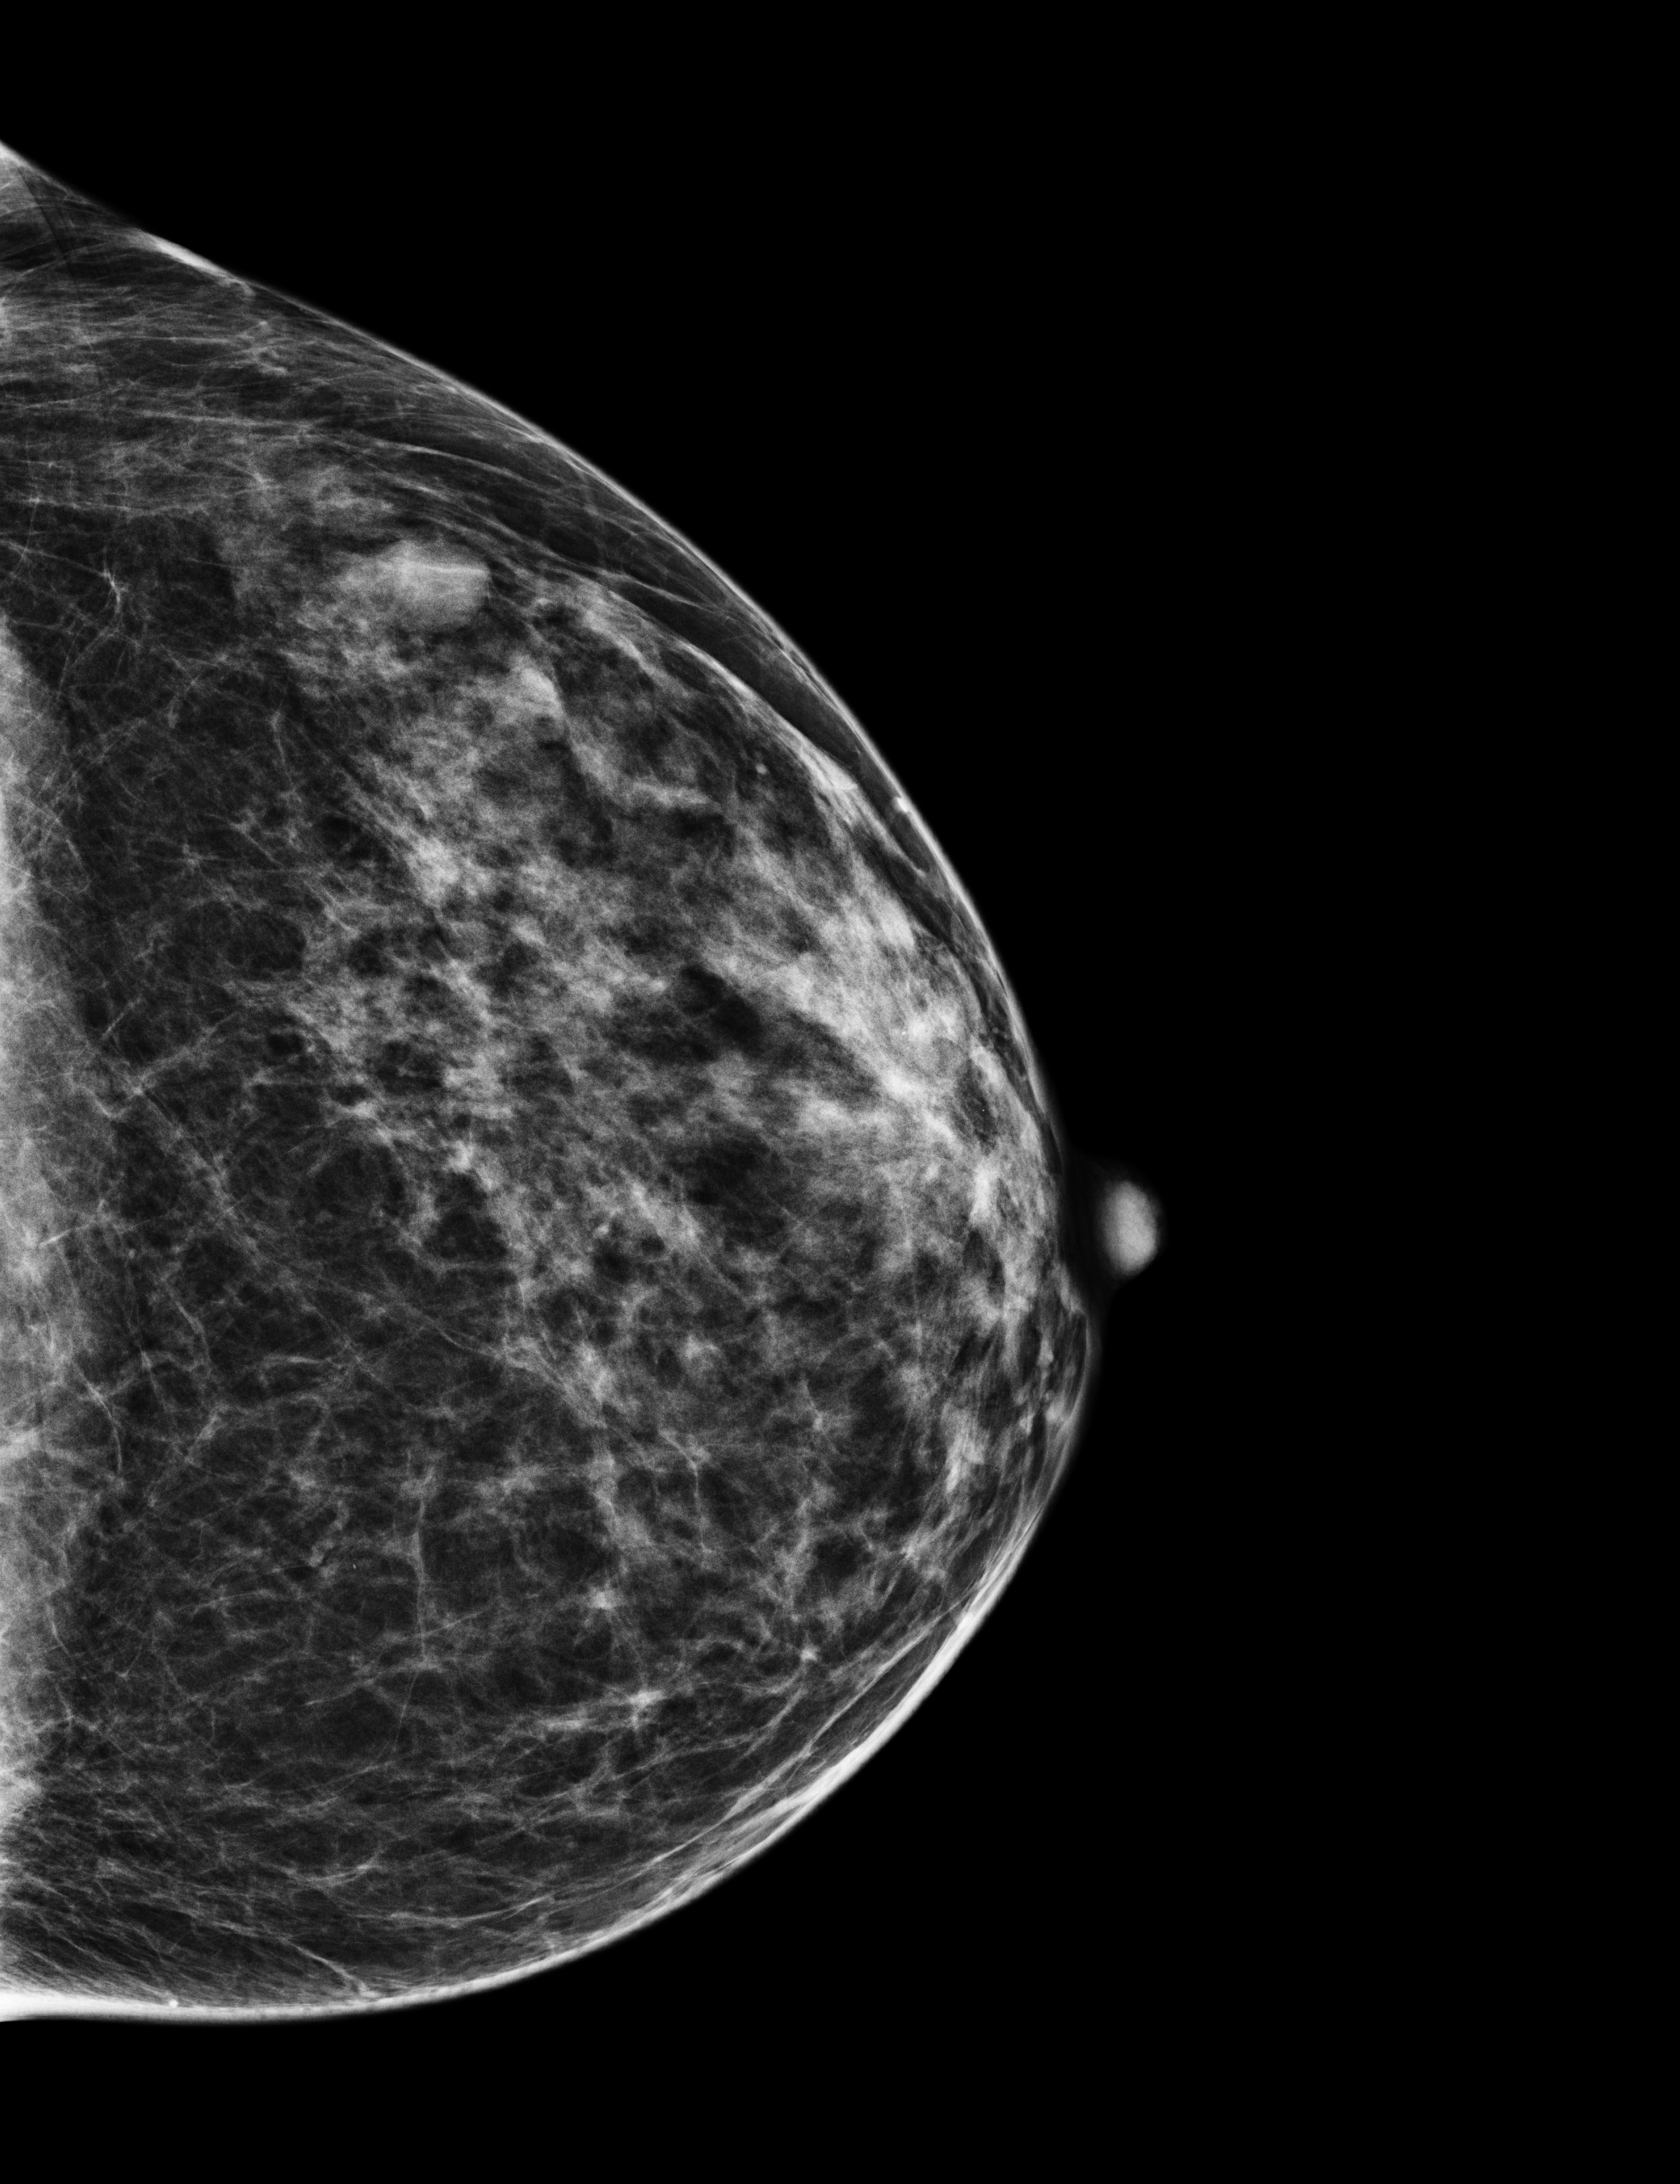
Annual screening mammography examination; compressed breast thickness 46 mm; system: Selenia Dimensions. Patient: female, 50 years.
Image type: full-field digital mammogram. Breast: left. Projection: craniocaudal (CC) view. BI-RADS breast density category at the screening exam (both breasts, scale 1–4): 3. Final BI-RADS assessment for this screening round (tomosynthesis exam, both breasts): category 1. Recall: no recall after this screen.